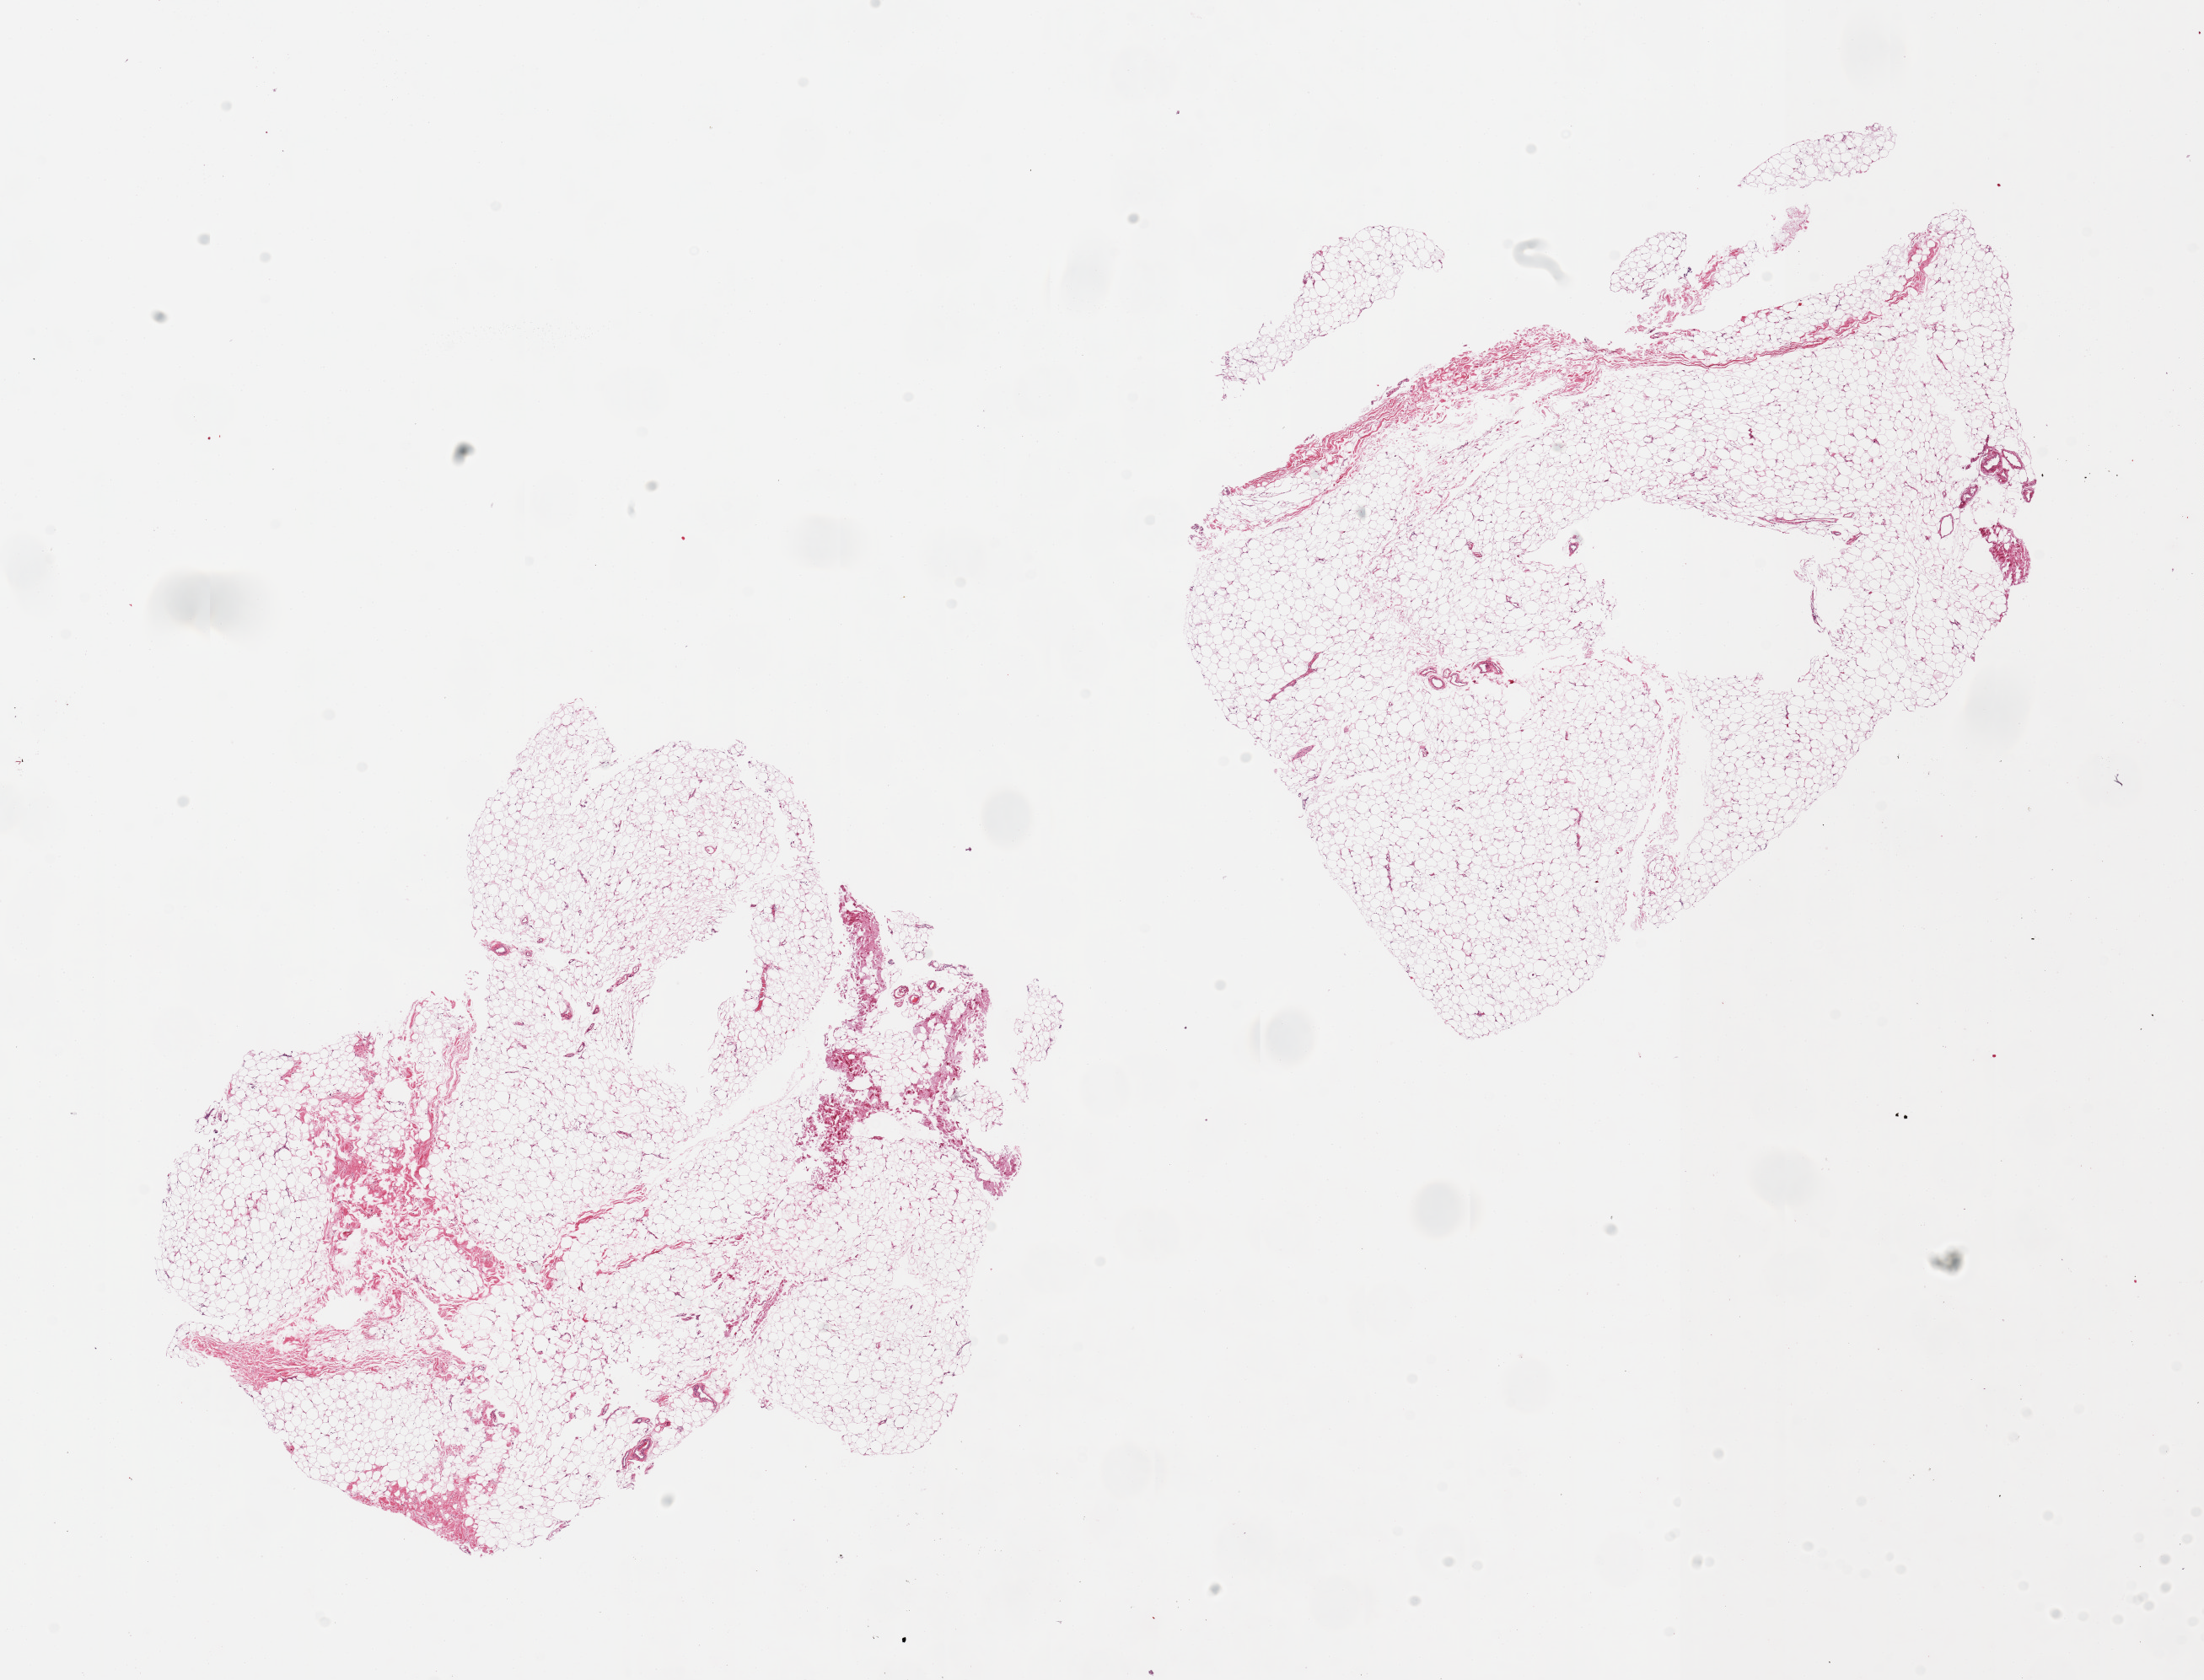
Whole-slide image, hematoxylin and eosin (H&E) stain, whole scanned area (about 20.7 x 15.8 mm) shown as a low-resolution overview, PAXgene-fixed paraffin-embedded (PFPE) section, target tissue: breast, tissue donor sample.
* review note (as recorded): 2 pieces, fibroadipose elements only; no ductal elements